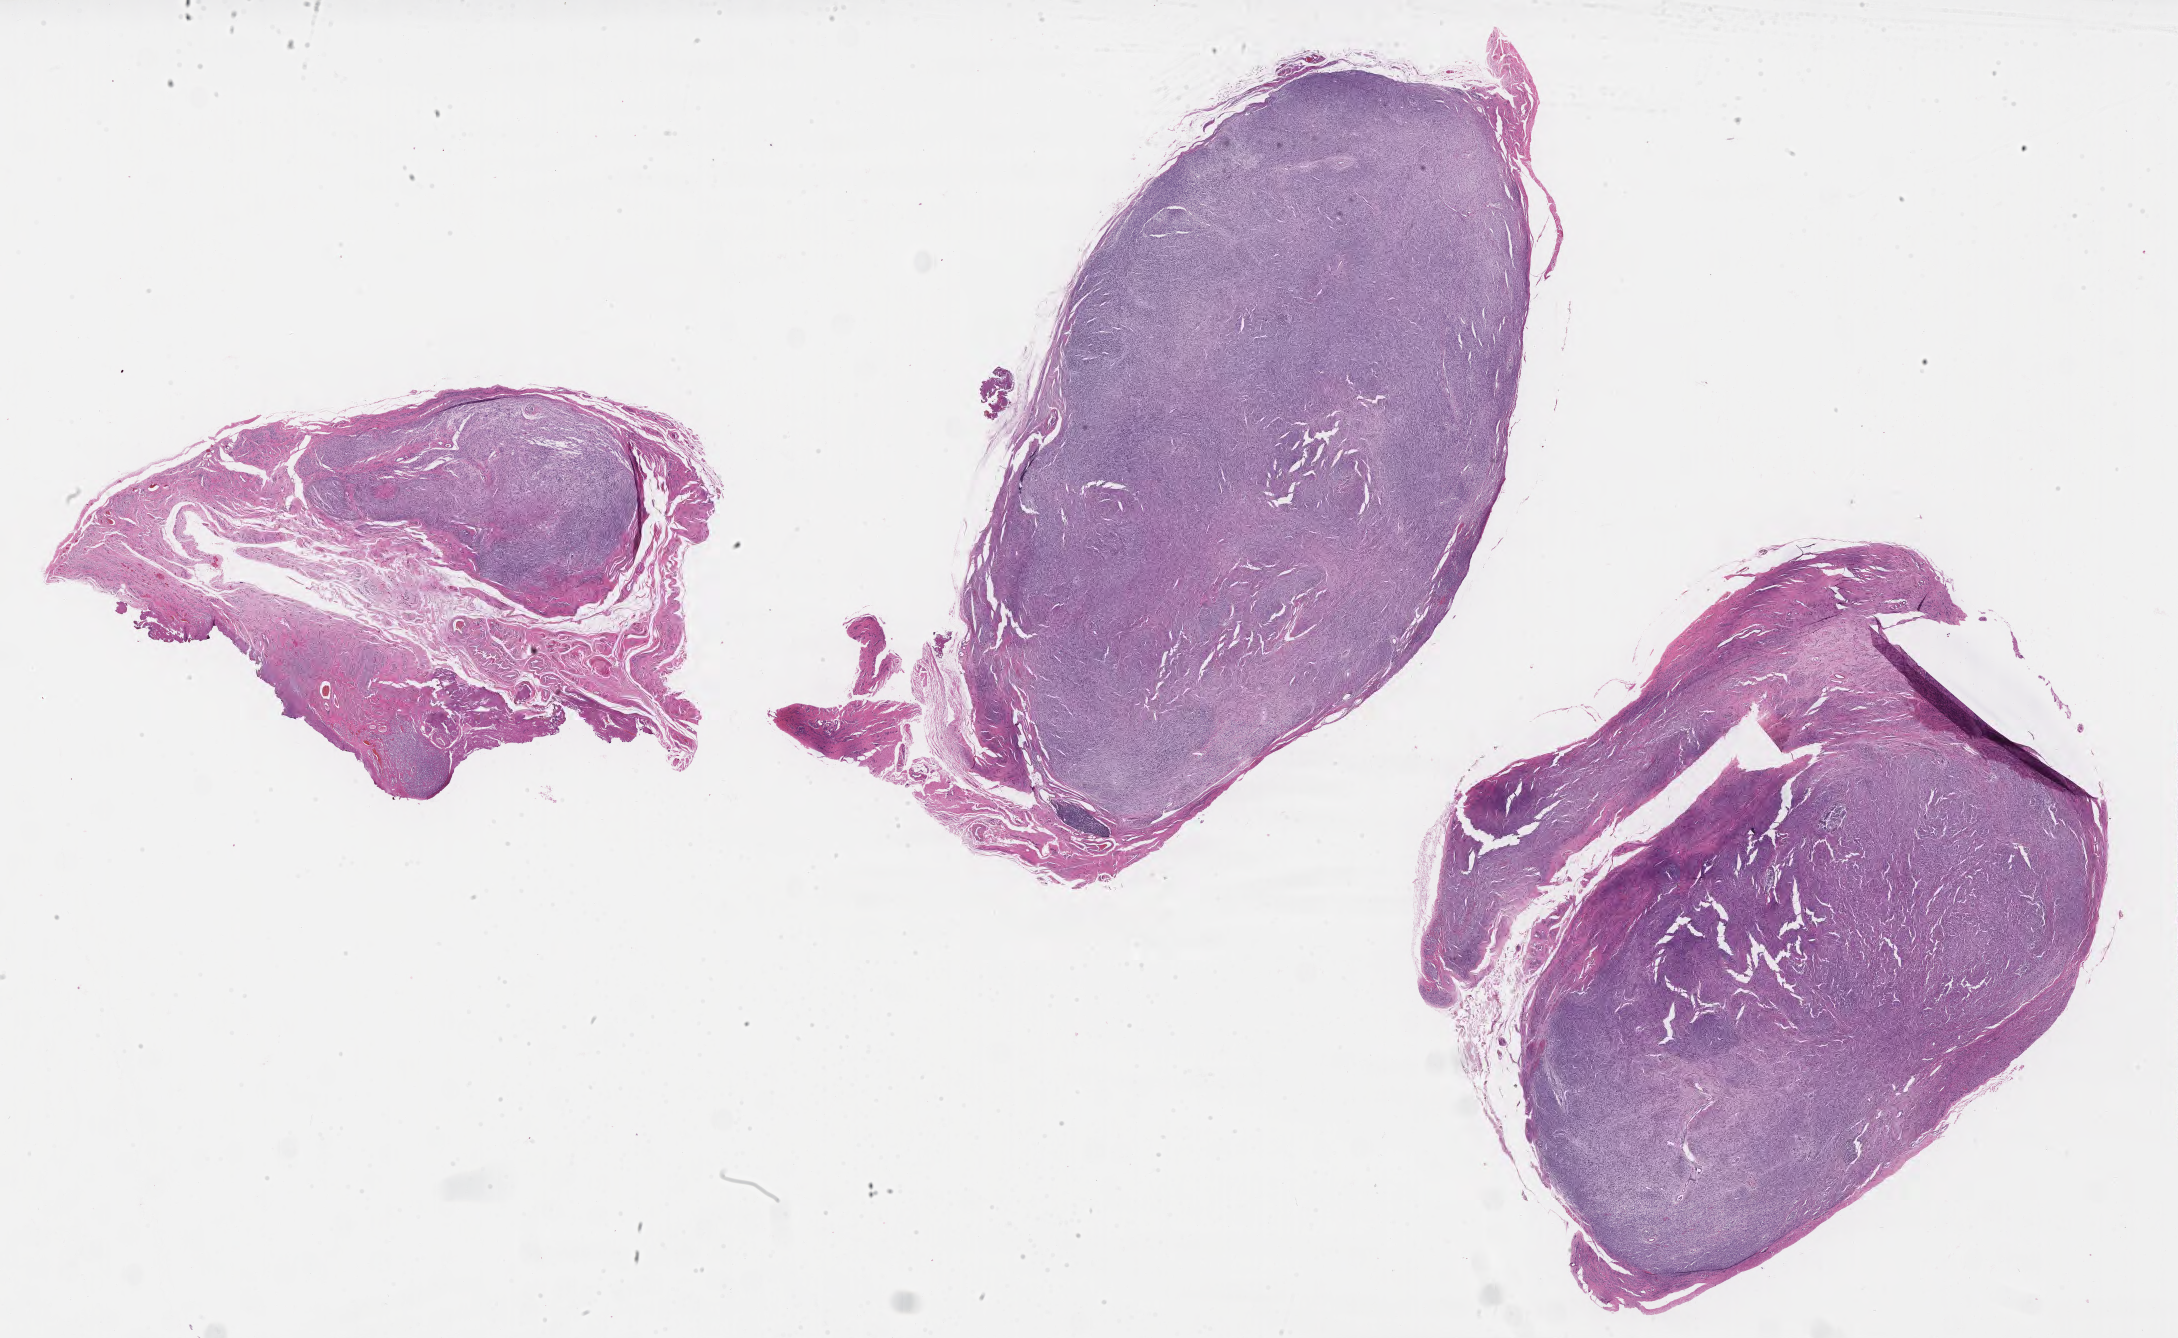
H&E whole-slide image of tumor tissue from the epididymis — a low-resolution overview of the entire scanned area, about 35.2 x 21.6 mm; formalin-fixed paraffin-embedded section. Male patient, age 273 days.
Recorded diagnosis: Embryonal rhabdomyosarcoma, NOS.